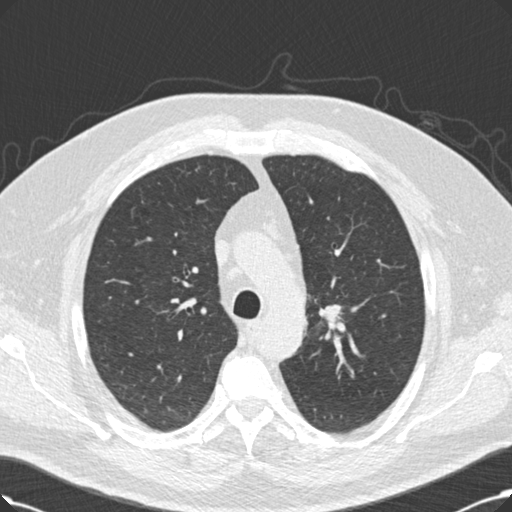
Low-dose screening chest CT, one axial slice; slice 160 of 214 in the series (ordered by position); reconstruction kernel B30f; 120 kVp; lung window (W 1500 / L -600 HU); 2 mm slice thickness; 512 × 512 image matrix, field of view 365 × 365 mm.
Structures marked on this image (expert manual segmentation):
- lesion 1 (tumor): bounding box (x1, y1, x2, y2) in pixels: (319, 305, 341, 329)